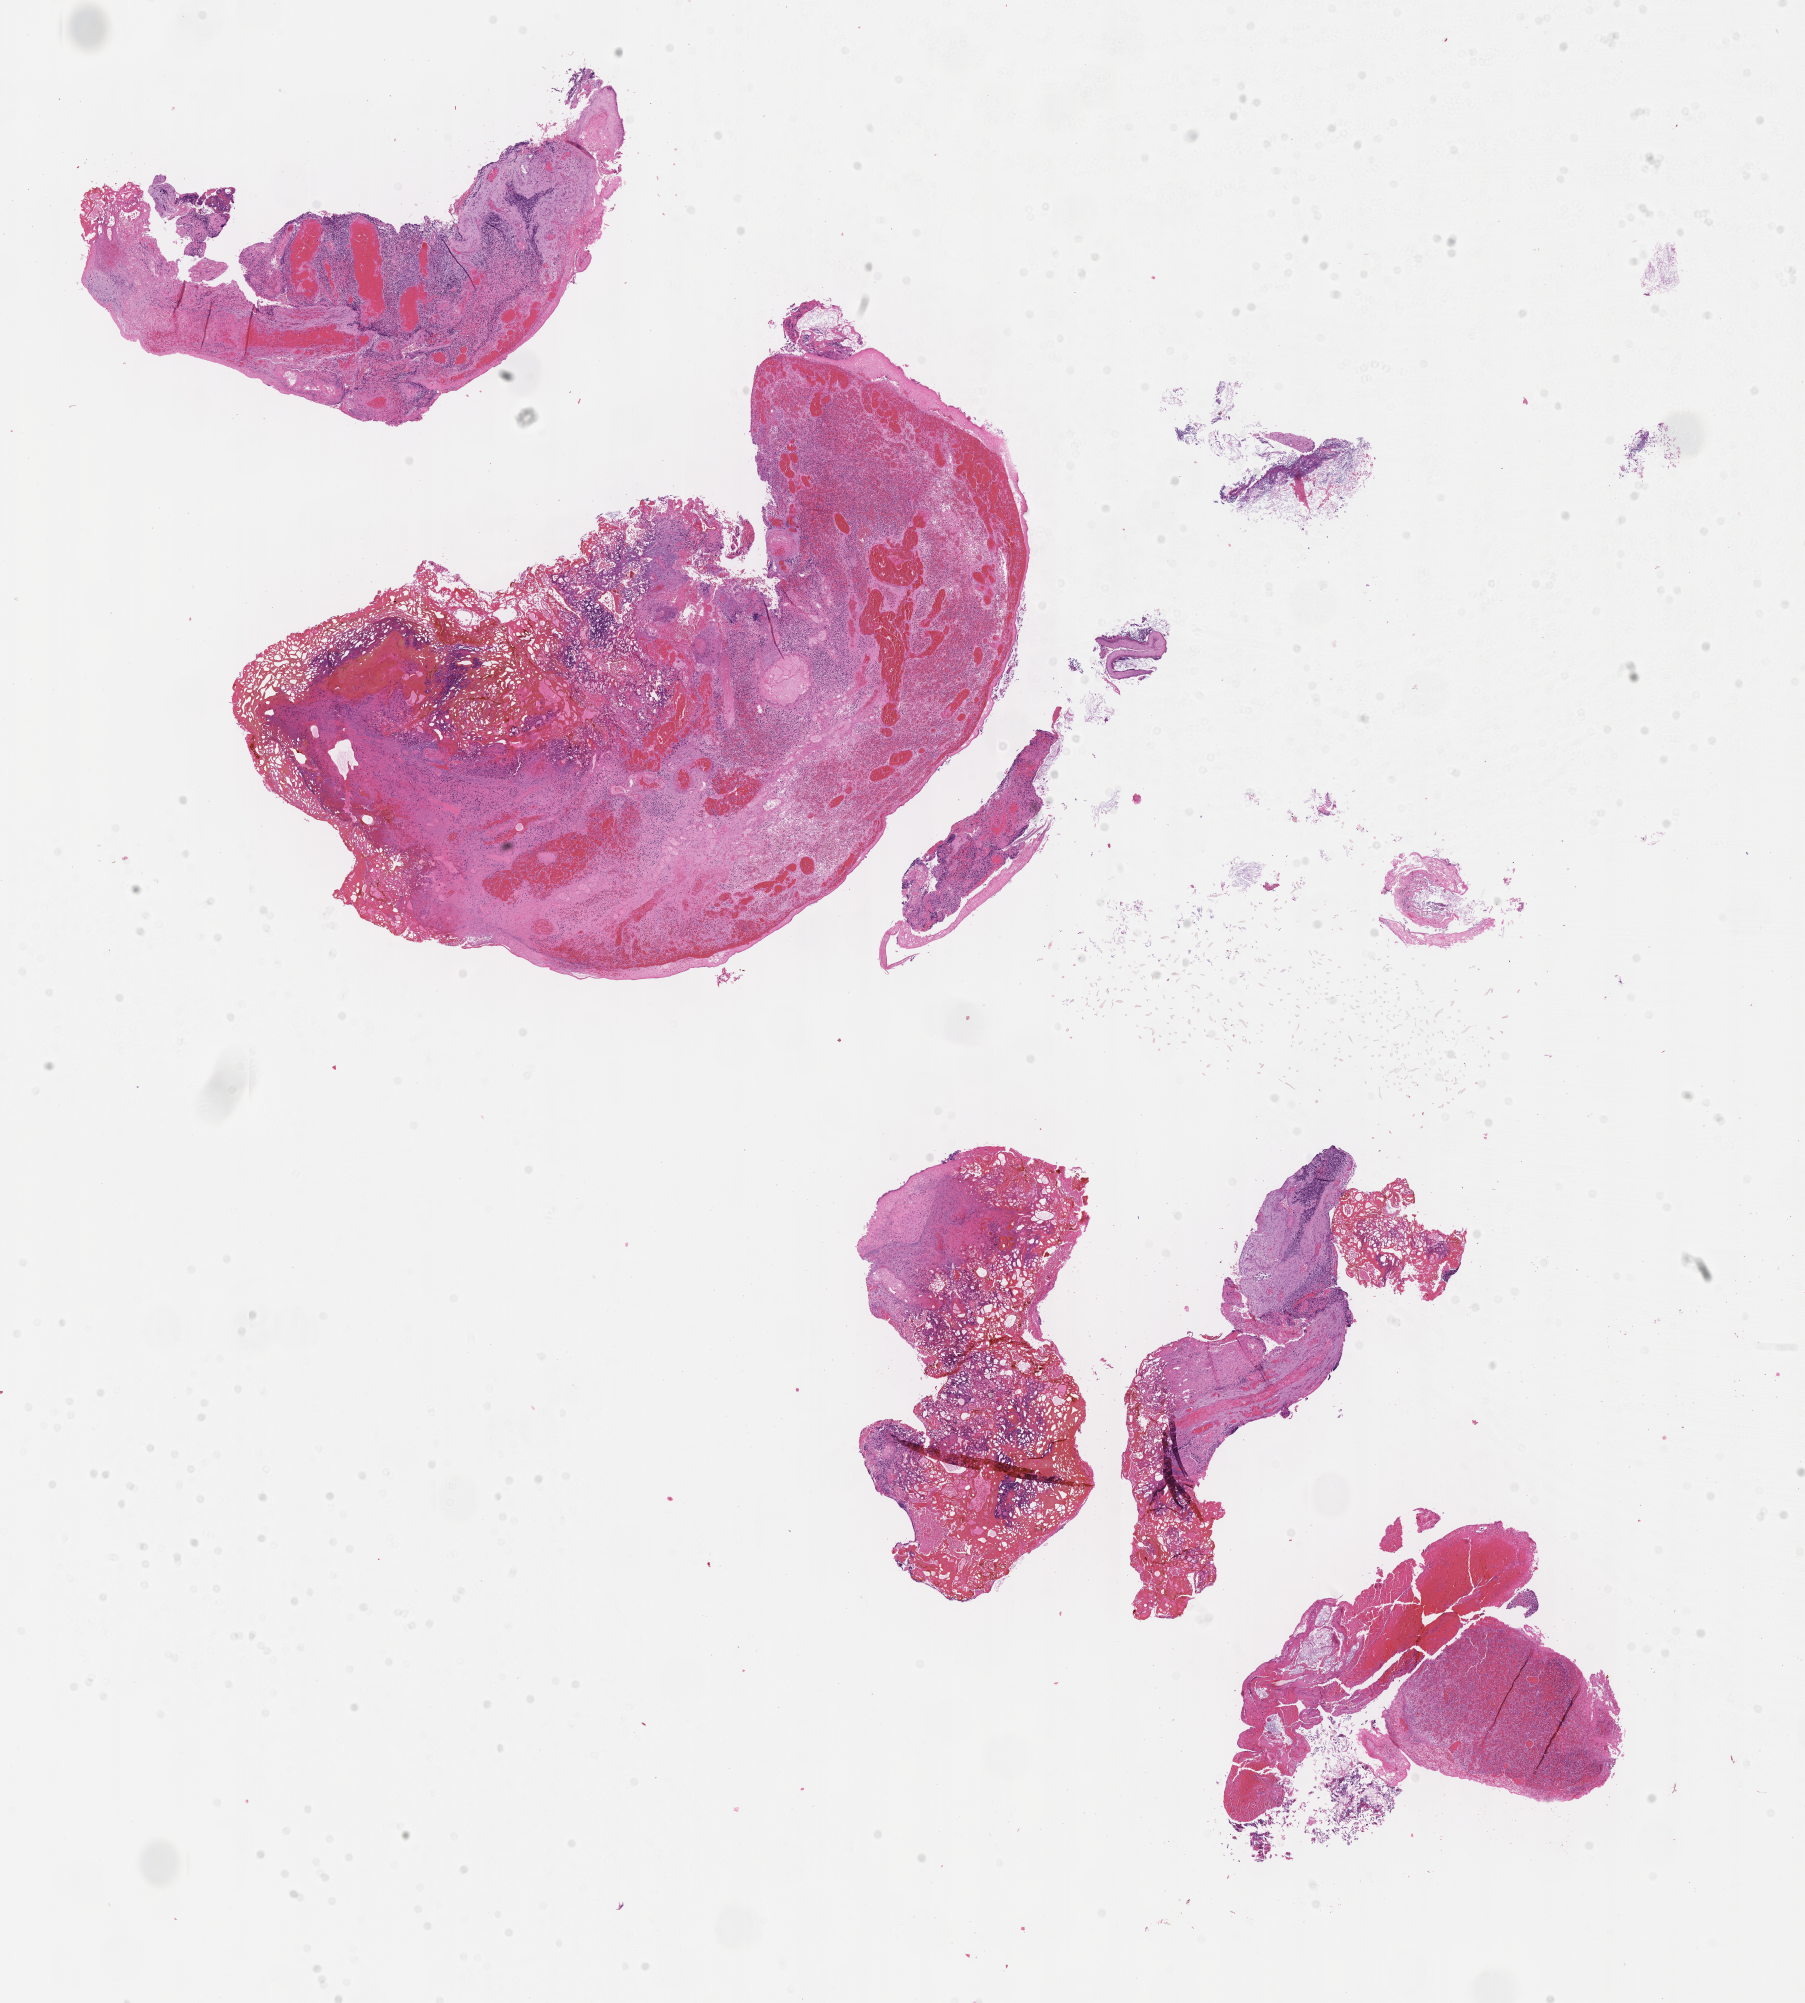
Digitized hematoxylin and eosin (H&E)-stained section of tumor tissue — a low-resolution overview of the entire scanned area, about 14.6 x 16.2 mm. FFPE section. Site: soft tissue, ear-right. Patient: male, age 4.1 years at diagnosis.
* stage (as recorded): 2
* diagnosis: rhabdomyosarcoma; histological classification: rhabdomyosarcoma nos
* metastatic status at presentation (as recorded): non-metastatic (unconfirmed)
* primary site (case record): middle ear (PM)